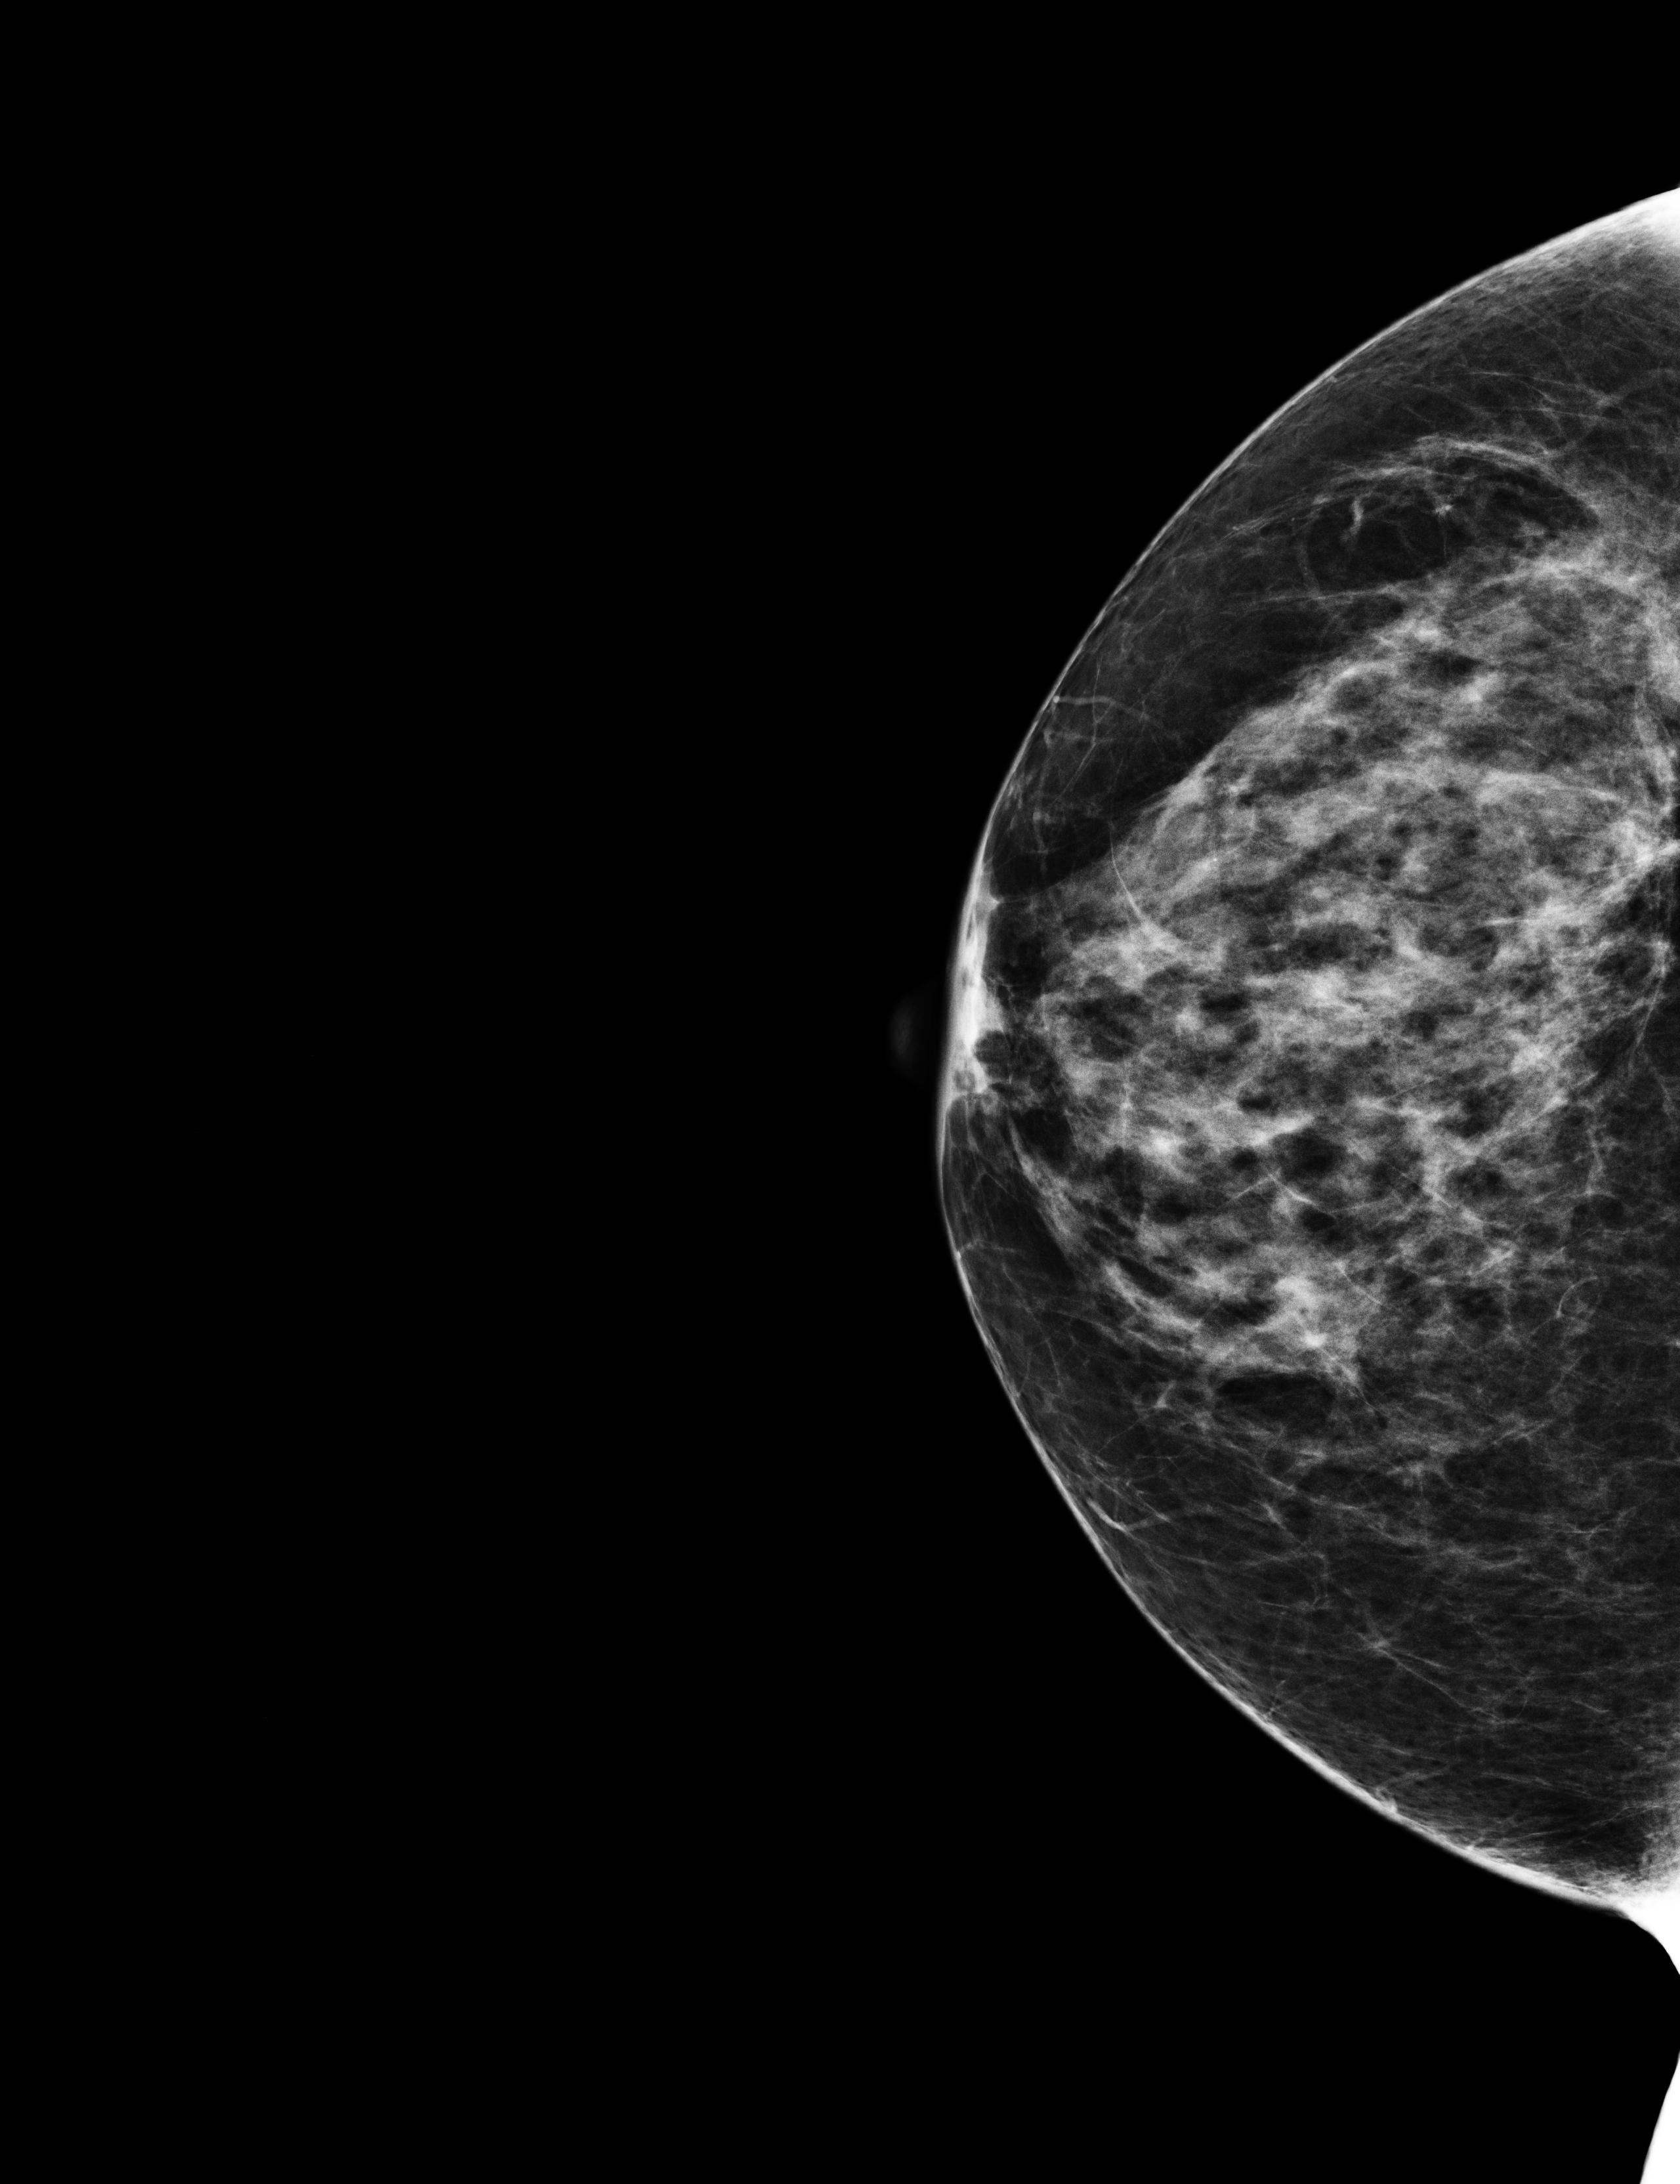
Screening examination, compressed breast thickness 54 mm, system: Selenia Dimensions. Female patient, age 59 years.
Image type: full-field digital mammogram. Breast: right. Projection: craniocaudal (CC) view.